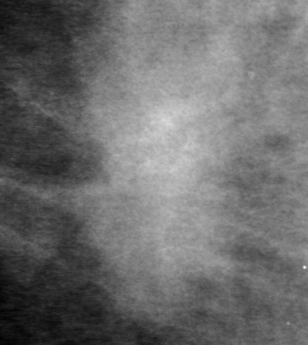
Crop from a digitized film mammogram around one marked abnormality, right breast, CC view, BI-RADS breast density category 3 (scale 1–4).
Mass, shape irregular, margins ill defined; BI-RADS assessment category 0 (incomplete: needs additional imaging); pathology (as recorded): malignant.